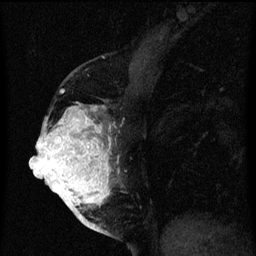
Breast MRI (dynamic contrast-enhanced), one sagittal slice; dynamic contrast-enhanced series, image 2 of 3 at this slice position (ordered by acquisition); 1.5 T; TE 4.2 ms, TR 8 ms; 2 mm slice thickness; 256 × 256 image matrix. Patient: female, 56 years.
Annotated regions visible in this slice (semi-automatic segmentation, software-assisted and operator-edited):
- analysis volume of interest (the breast-tissue region the enhancement analysis was run in; not a lesion): bounding box (x1, y1, x2, y2) in pixels: (40, 104, 123, 219)
- tumour enhancement mask (voxels above the 70 % enhancement threshold inside the analysis volume of interest): (40, 106, 115, 219)